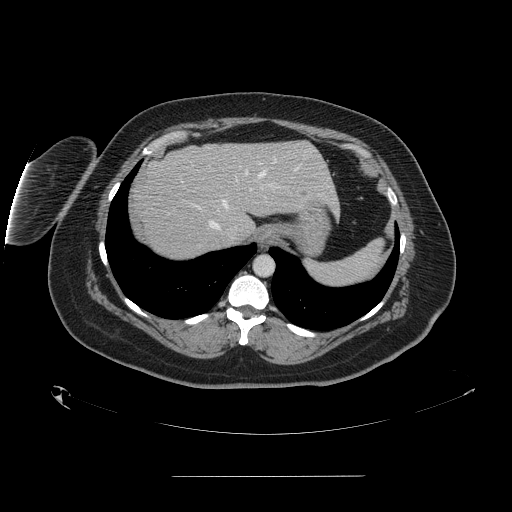
Contrast-enhanced abdominal CT, one axial slice; position 126 of 164 along the scan axis; 120 kVp; intravenous contrast given; soft-tissue window (W 400 / L 40 HU); 2.5 mm slice thickness; 512 × 512 image matrix, field of view 495 × 495 mm. Female patient, age 52 years. Case-level facts recorded for this patient, not image findings: diagnosis: colorectal cancer liver metastases, imaged before liver resection.
Annotated regions visible in this slice (outlined manually by an expert reader):
- hepatic veins: box from (x=208, y=170) to (x=265, y=238) px
- liver: (x=132, y=141)–(x=337, y=260)
- planned liver remnant (the part of the liver to remain after resection): (x=171, y=141)–(x=337, y=227)
- portal vein (with intrahepatic branches): (x=181, y=181)–(x=272, y=189)